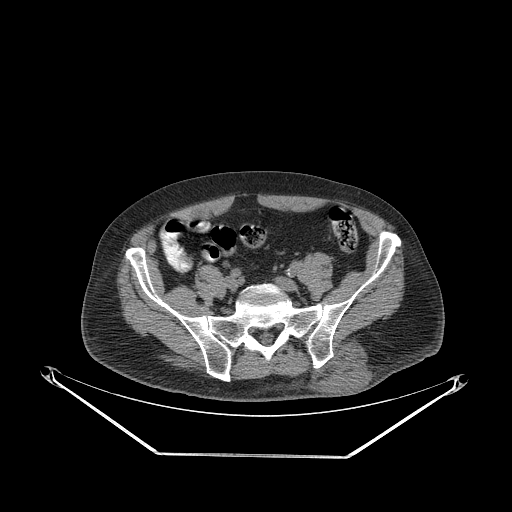
CT of an extremity soft-tissue mass (from a PET/CT study), one axial slice. Slice 79 of 267 in the series (ordered by position). Reconstruction kernel STANDARD. 140 kVp. Soft-tissue window (W 400 / L 40 HU). 3.75 mm slice thickness. 512 × 512 image matrix, field of view 500 × 500 mm. Male patient. Case-level facts recorded for this patient, not image findings: histological type: leiomyosarcoma; grade: intermediate; site of the primary tumour: left pelvis.
Annotated regions visible in this slice (expert contour drawn on MRI and transferred to this co-registered scan by the dataset authors):
- gross tumour volume (mass): box from (x=315, y=343) to (x=371, y=396) px